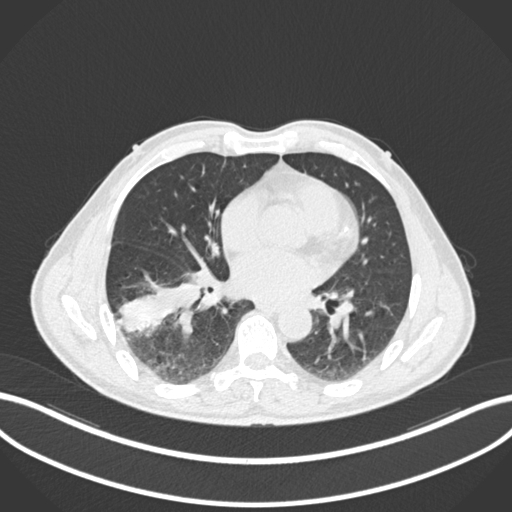
Chest CT, one axial slice; slice 86 of 208 in the series (ordered by position); lung window (W 1500 / L -600 HU); 1 mm slice thickness; 512 × 512 image matrix, field of view 400 × 400 mm. Male patient, age 58 years. From the clinical record (not read from this slice): clinical TNM (as recorded): T3 N0 M0.
Outlined on this slice (bounding box drawn by a radiologist):
- lung tumour (recorded histology: squamous cell carcinoma): box from (x=110, y=271) to (x=201, y=335) px